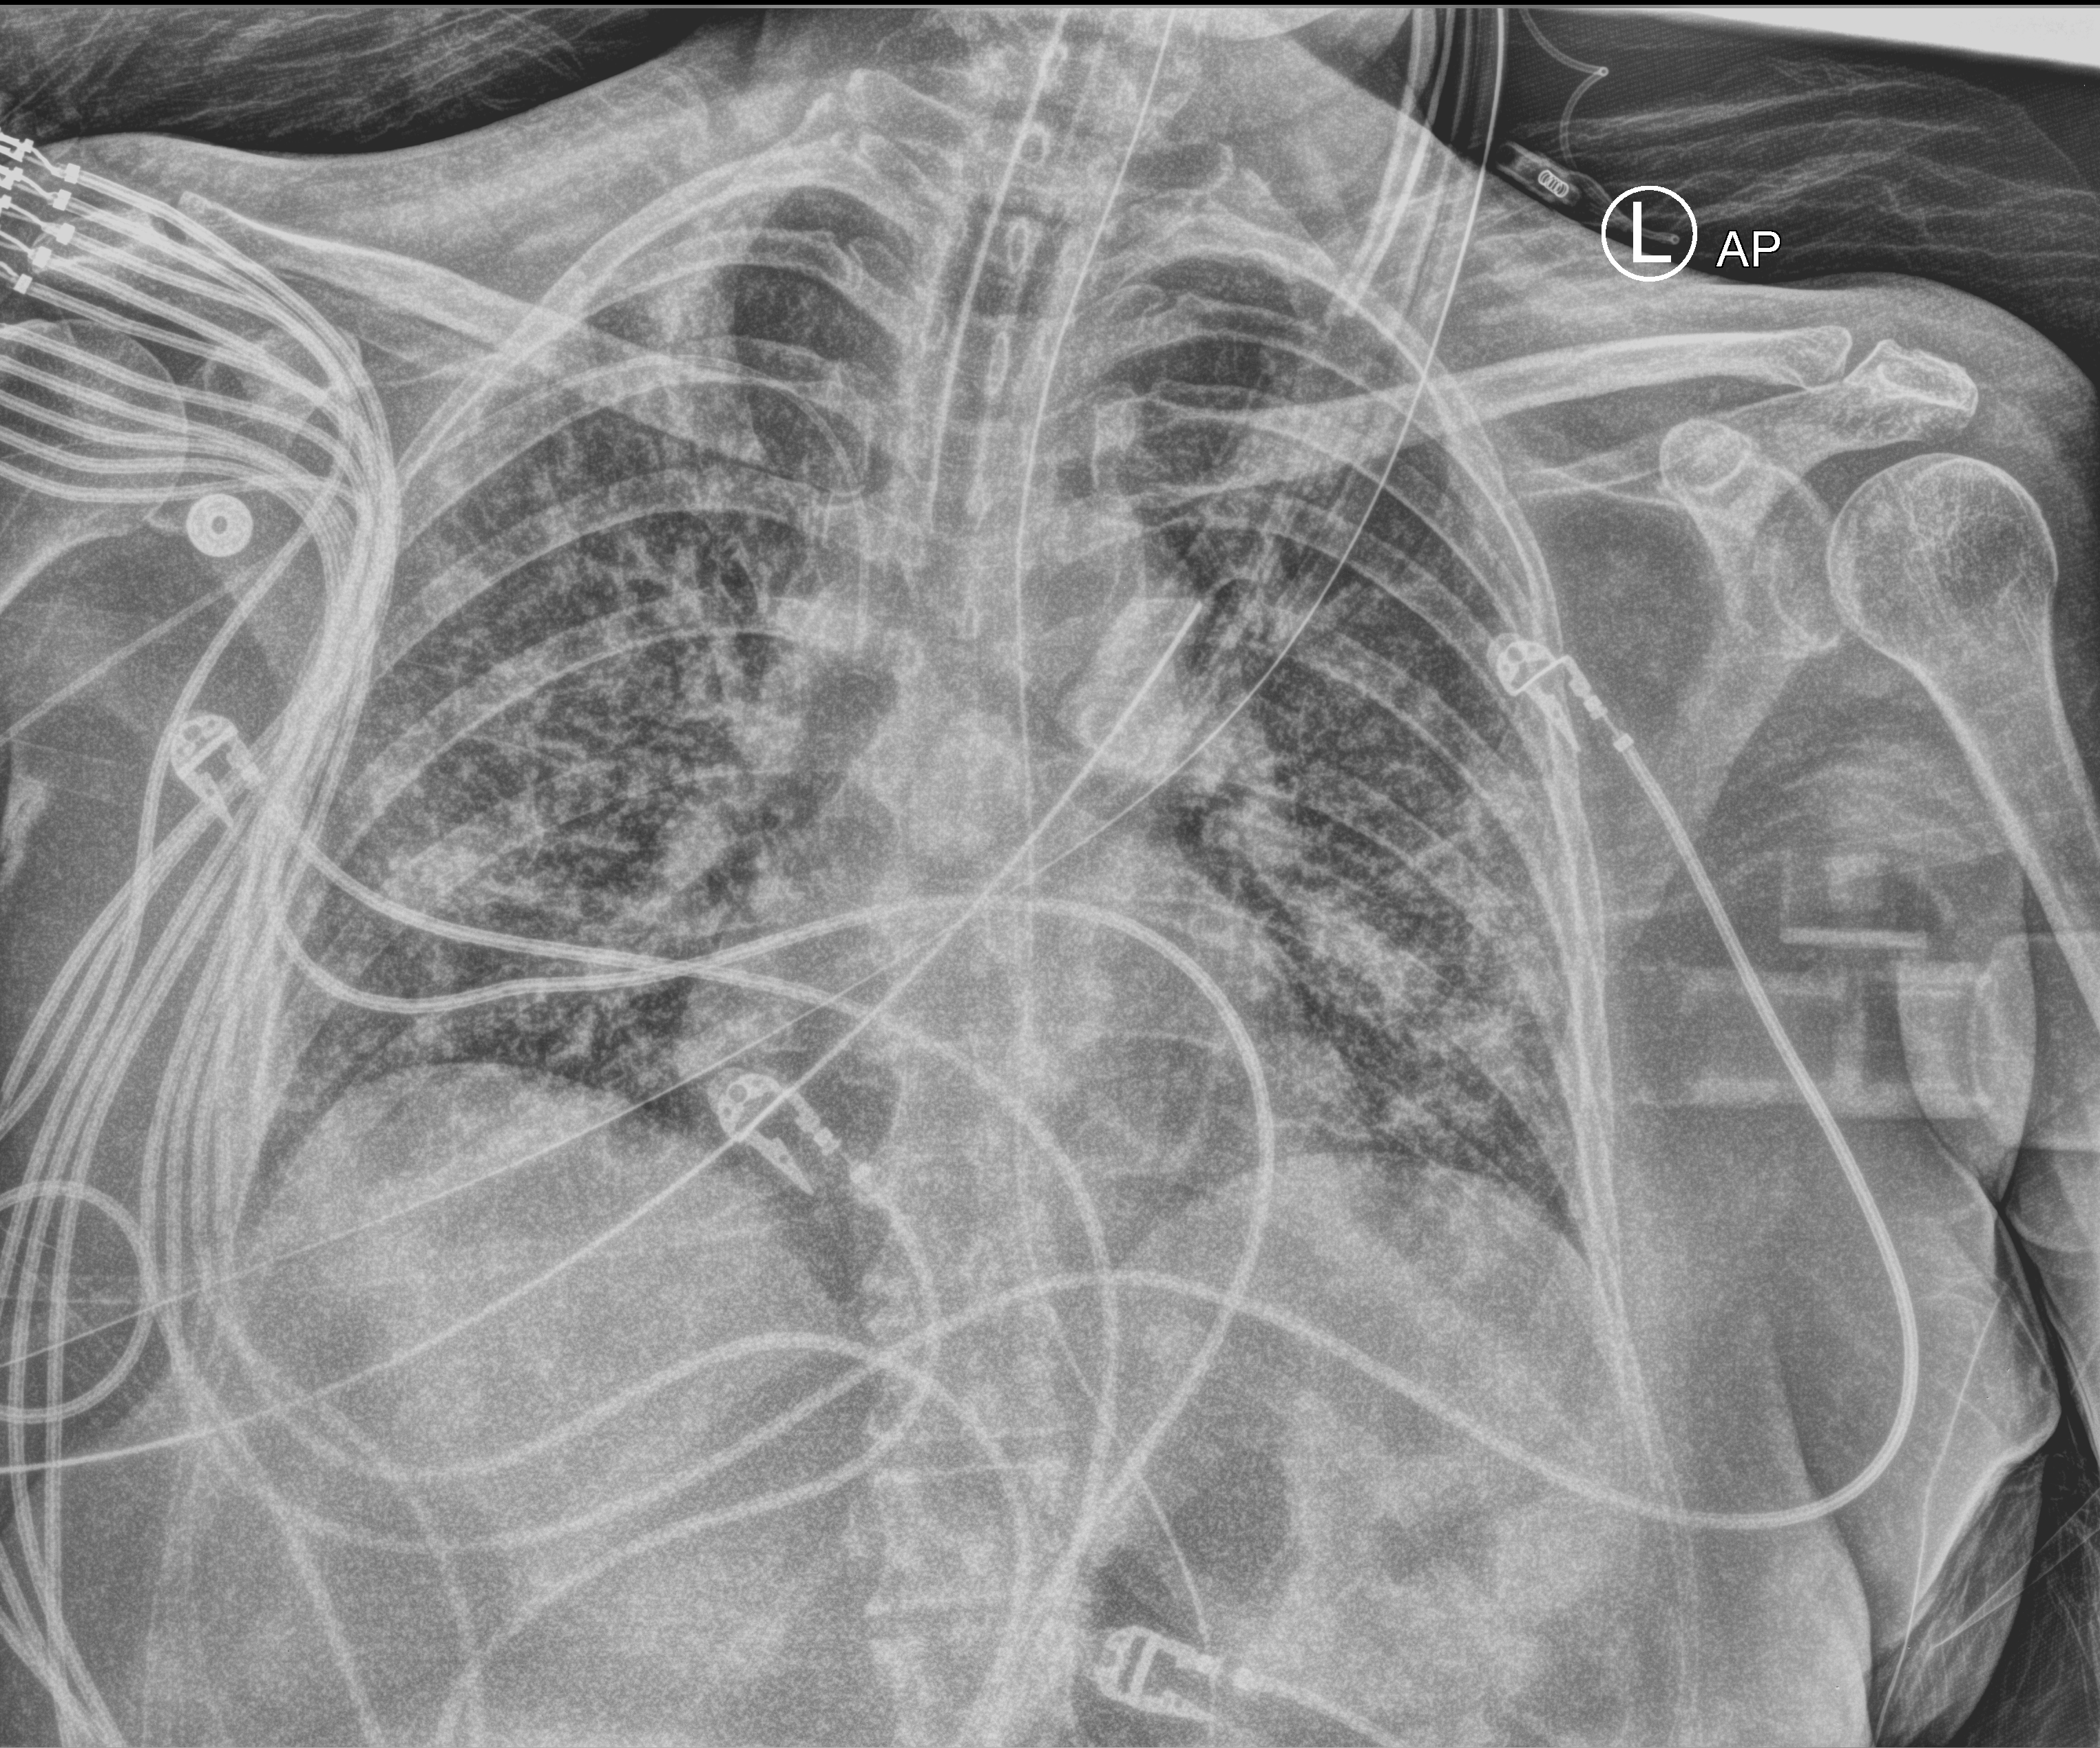
Chest X-ray (portable), anteroposterior (AP) projection. Female patient hospitalised with COVID-19, age 60–74 years.
Hospital-stay facts (about this admission, not read from this image; timing relative to this image not recorded): length of hospital stay: 43 days; other chronic lung disease (admission record): no; mechanically ventilated during this hospital stay: yes.